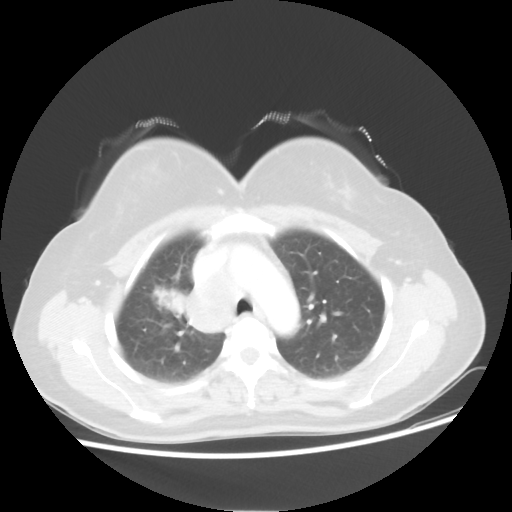
Chest CT, one axial slice. Slice 37 of 50 in the series (ordered by position). Reconstruction kernel STANDARD. Lung window (W 1500 / L -600 HU). 512 × 512 image matrix, field of view 360 × 360 mm. Patient: female, 40 years. From the clinical record (not read from this slice): clinical TNM (as recorded): T1c N3 M0; histopathological grade: G3.
Annotated regions visible in this slice (bounding box drawn by a radiologist):
- lung tumour (recorded histology: small cell carcinoma): bounding box <152,284,184,319> (left, top, right, bottom; pixels)